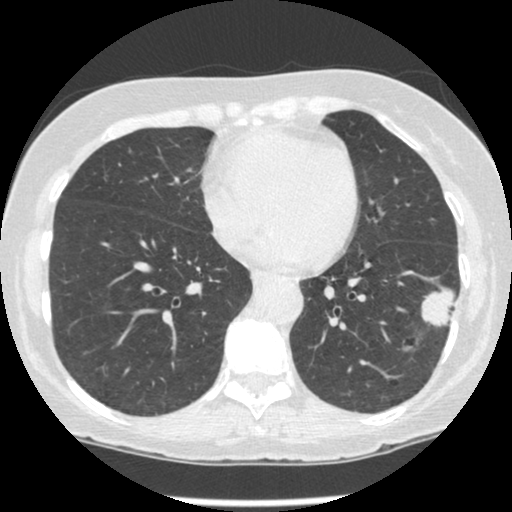
Low-dose screening chest CT, one axial slice; slice 95 of 247 in the series (ordered by position); reconstruction kernel STANDARD; lung window (W 1500 / L -600 HU); 512 × 512 image matrix.
Outlined on this slice (manually delineated by an expert):
- lesion 1 (tumor, lower lobe of left lung): box from (x=421, y=289) to (x=455, y=327) px